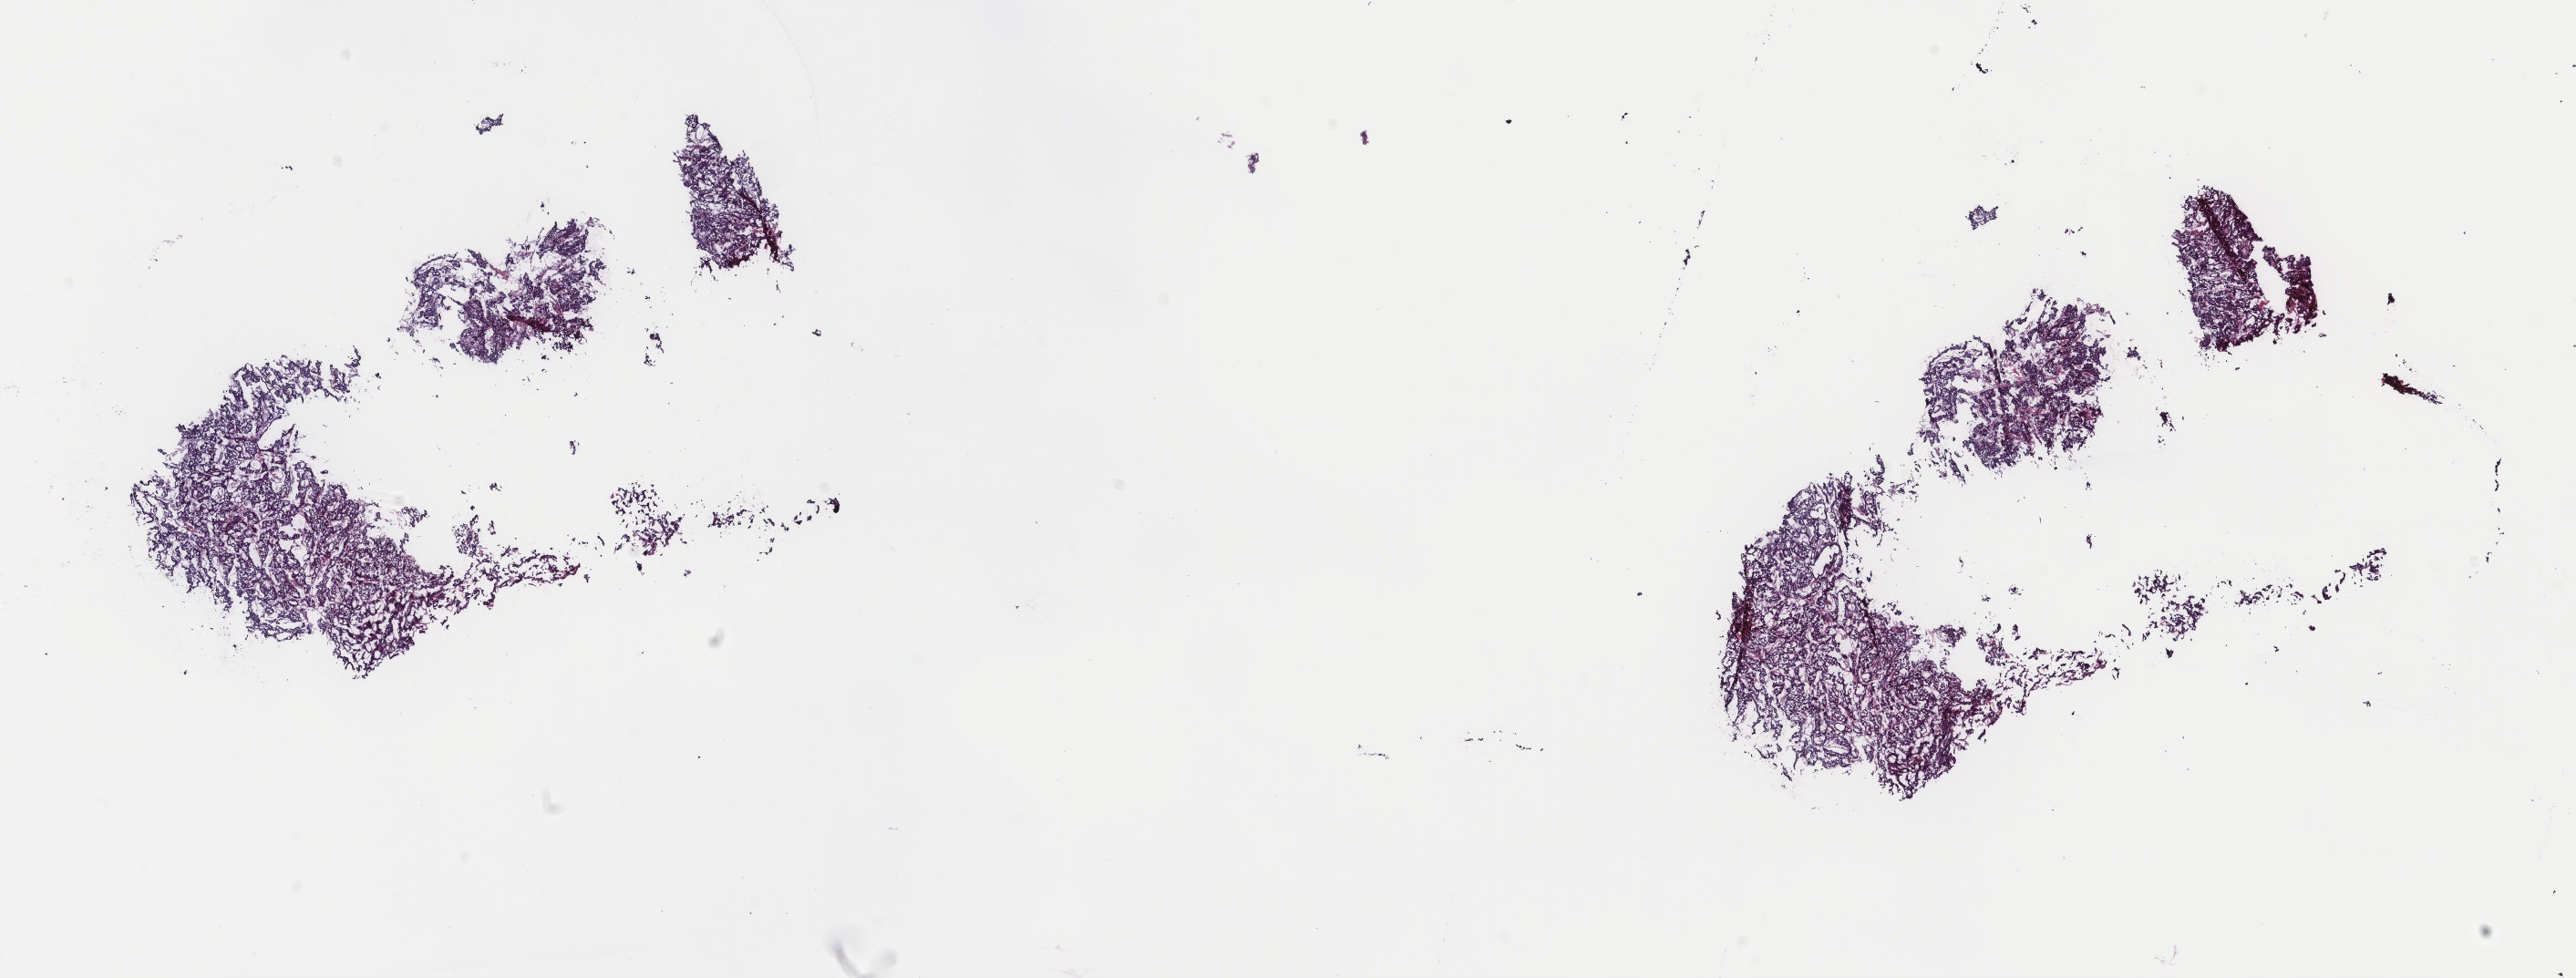
Digitized Hematoxylin and eosin (H&E) stained tissue section (whole slide) — whole scanned area (about 22.4 x 8.5 mm) shown as a low-resolution overview. Frozen section. Thyroid, primary tumour sample. Patient: female, age at initial diagnosis 51 years. Composition of this section per pathologist review: tumour cells 80%, tumour nuclei 95%, normal cells 0%, stromal cells 20%, necrosis 0%. Inflammatory infiltration, as recorded: lymphocyte infiltration 0%, monocyte infiltration 0%, neutrophil infiltration 0%.
* AJCC pathologic stage: II (7th edition)
* histologic diagnosis: Papillary carcinoma, follicular variant (thyroid gland)
* laterality: left